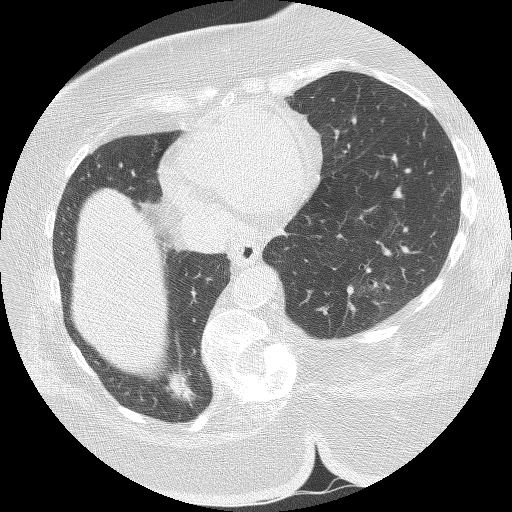
Chest CT (low-dose screening protocol), one axial image, first (baseline) screen, lung window (W 1500 / L -600 HU), 2.5 mm slice thickness, lung (sharp) reconstruction kernel (BONE), slice 102 of 151 in the series. Female, age 59 years at enrolment. Former smoker at enrolment.
Lesion marked by an expert reader, bounding box <143,348,204,419> (left, top, right, bottom; pixels). Reader record for this screening exam (exam-level; its link to the box is not recorded): non-calcified nodule or mass ≥4 mm, right lower lobe, 21 × 10 mm, spiculated (stellate) margins, soft tissue attenuation.